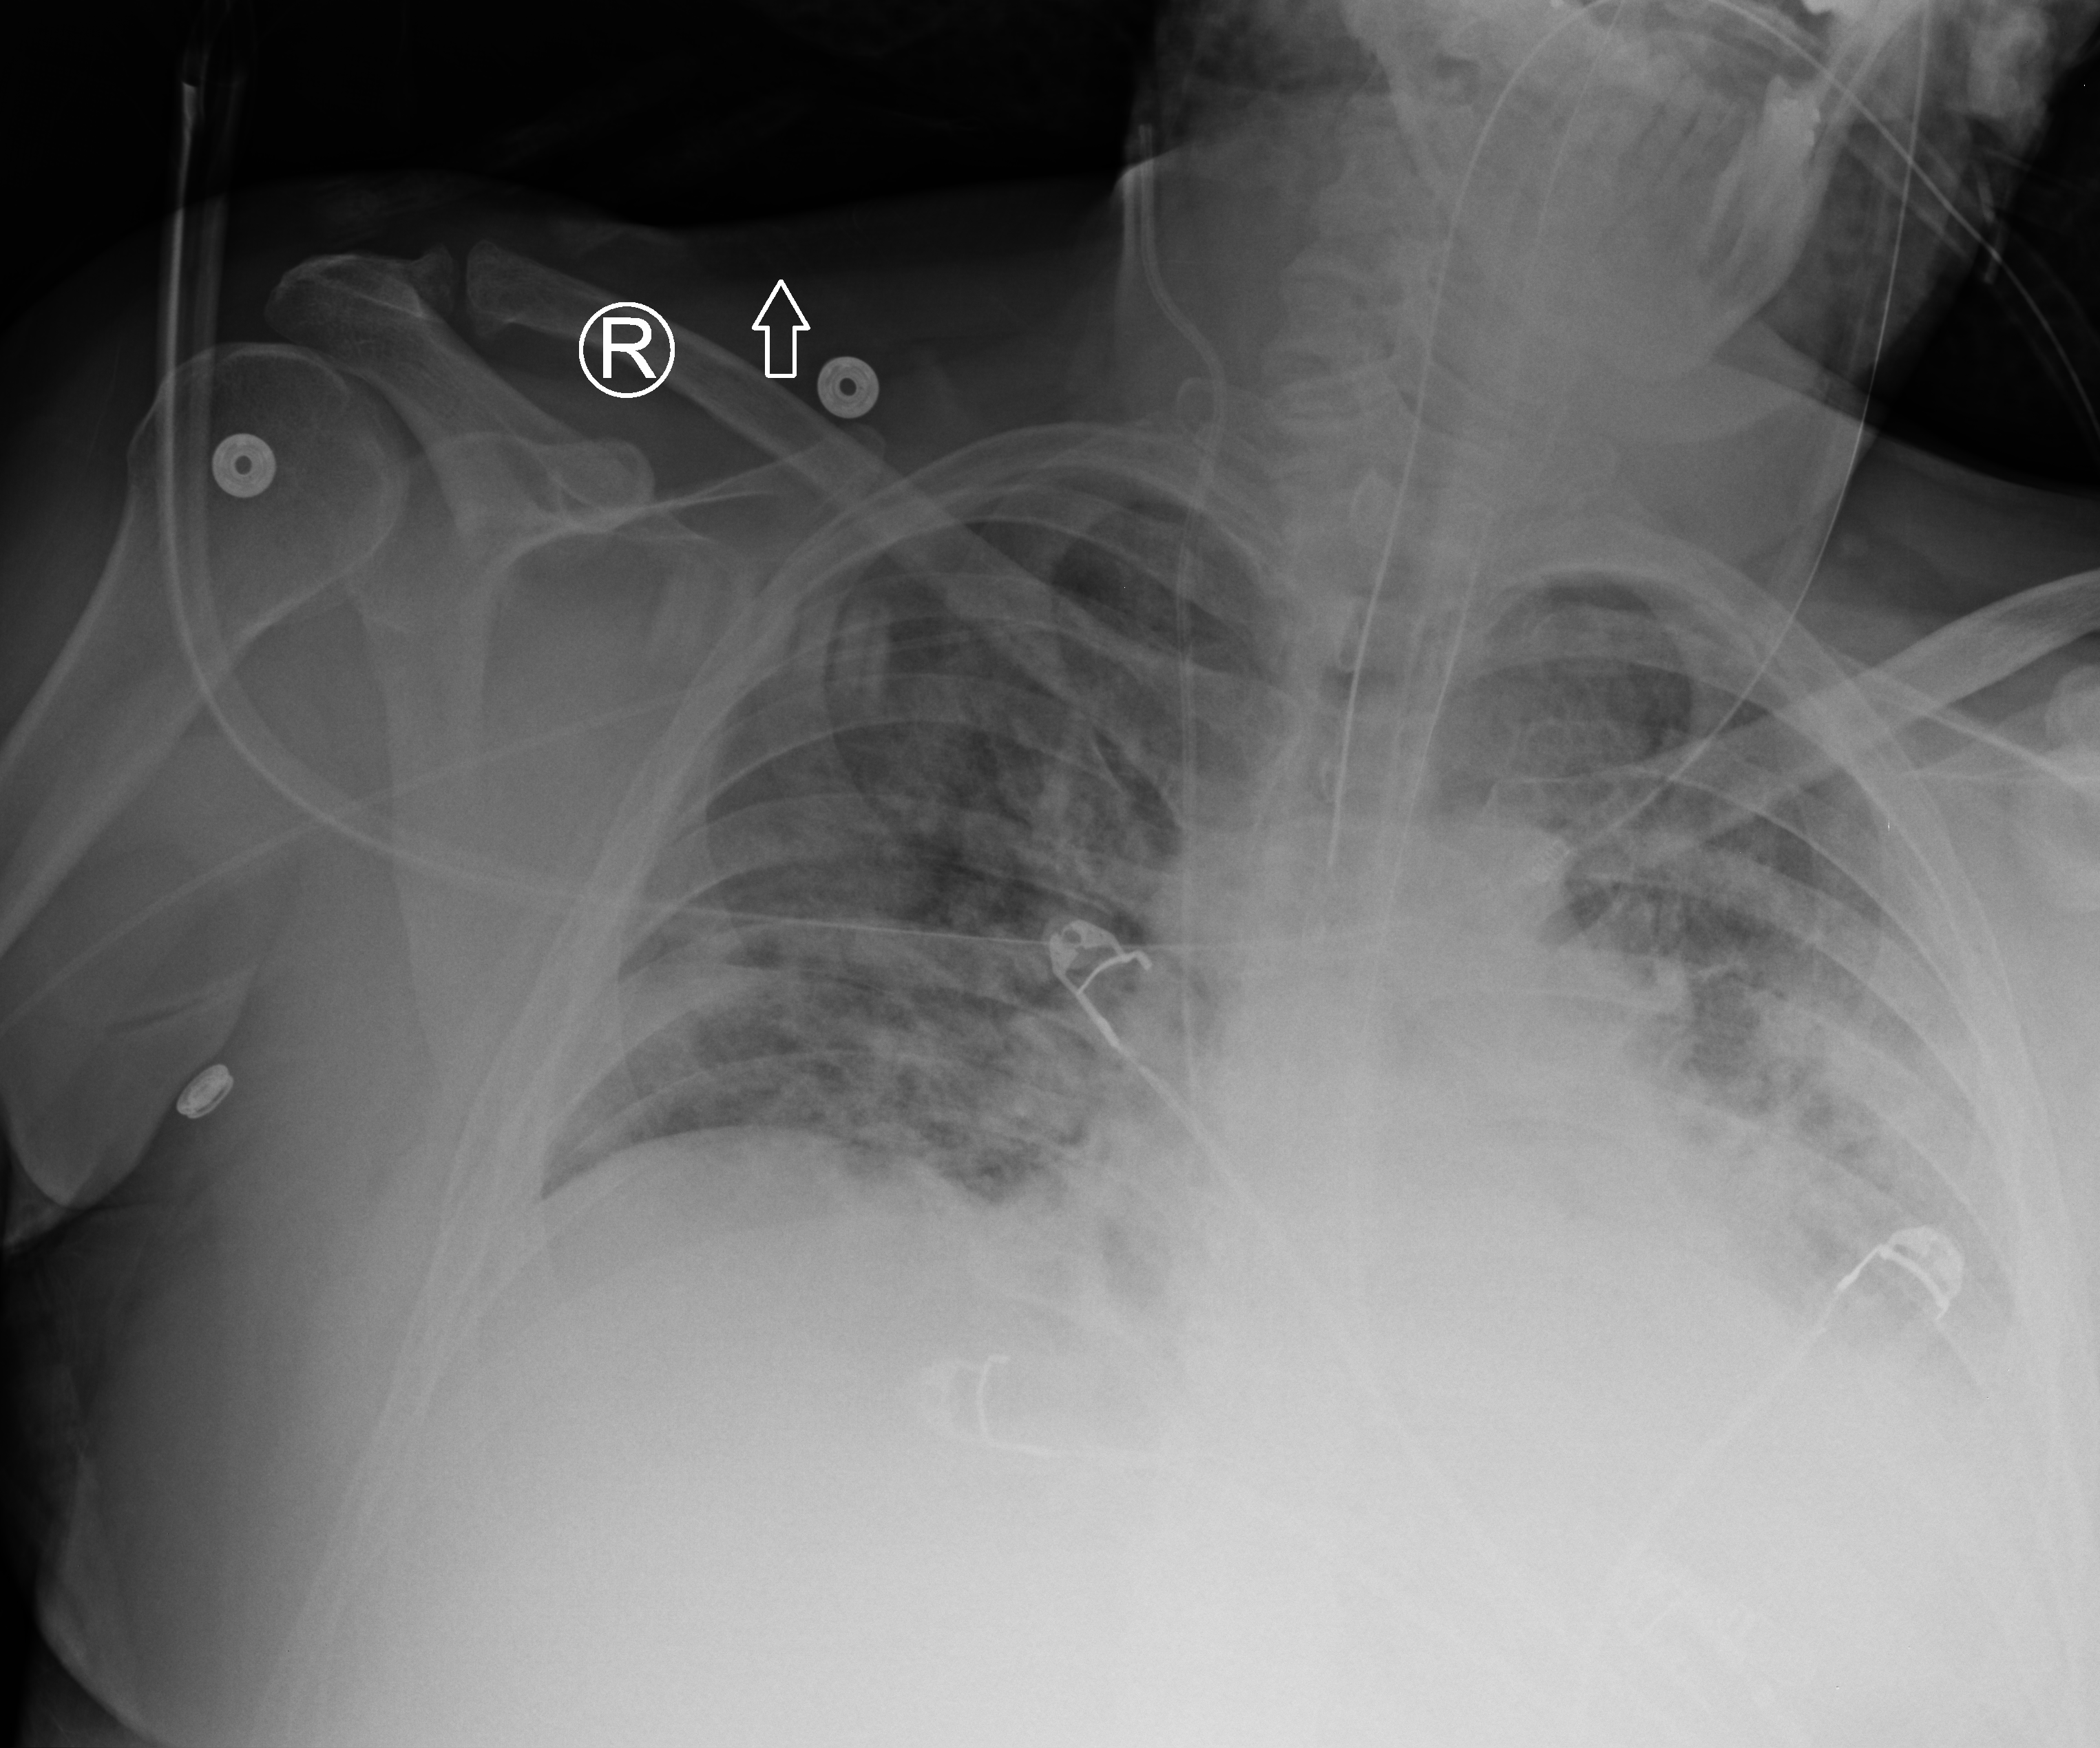
Bedside chest radiograph (computed radiography); anteroposterior (AP) projection. Patient hospitalised with COVID-19; male, aged 18–59 years.
Admission-level facts for this patient (not findings on this image; timing relative to this image not recorded): mechanically ventilated during this hospital stay: yes; COPD (admission record): no.